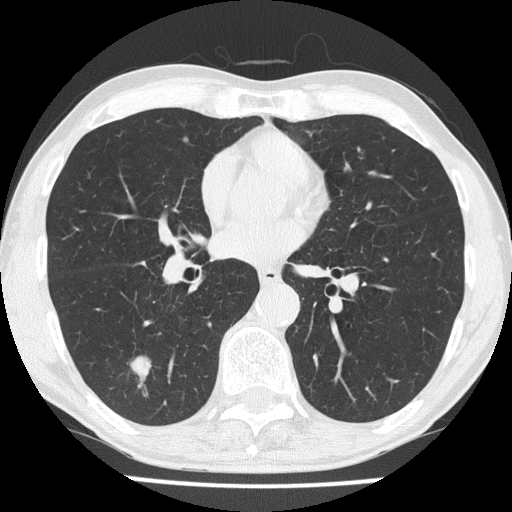
Low-dose screening chest CT, one axial slice; slice 80 of 186 in the series (ordered by position); lung window (W 1500 / L -600 HU); 2 mm slice thickness; 512 × 512 image matrix.
Structures marked on this image (manually delineated by an expert):
- lesion 1 (tumor, lower lobe of right lung): bounding box [x1, y1, x2, y2] px = [131, 356, 152, 381]